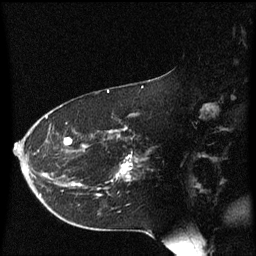
Breast MRI (dynamic contrast-enhanced), one sagittal slice; dynamic contrast-enhanced series, image 2 of 3 at this slice position (ordered by acquisition); 1.5 T; TE 4.2 ms, TR 8.4 ms; 256 × 256 image matrix. Female patient, age 54 years. Case-level facts recorded for this patient, not image findings: setting: breast cancer imaged before/during neoadjuvant chemotherapy; receptor status: HR-positive, HER2-negative.
Structures marked on this image (semi-automatically segmented with operator editing):
- analysis volume of interest (the breast-tissue region the enhancement analysis was run in; not a lesion): bounding box <102,130,142,191> (left, top, right, bottom; pixels)
- tumour enhancement mask (voxels above the 70 % enhancement threshold inside the analysis volume of interest): <119,156,133,181>